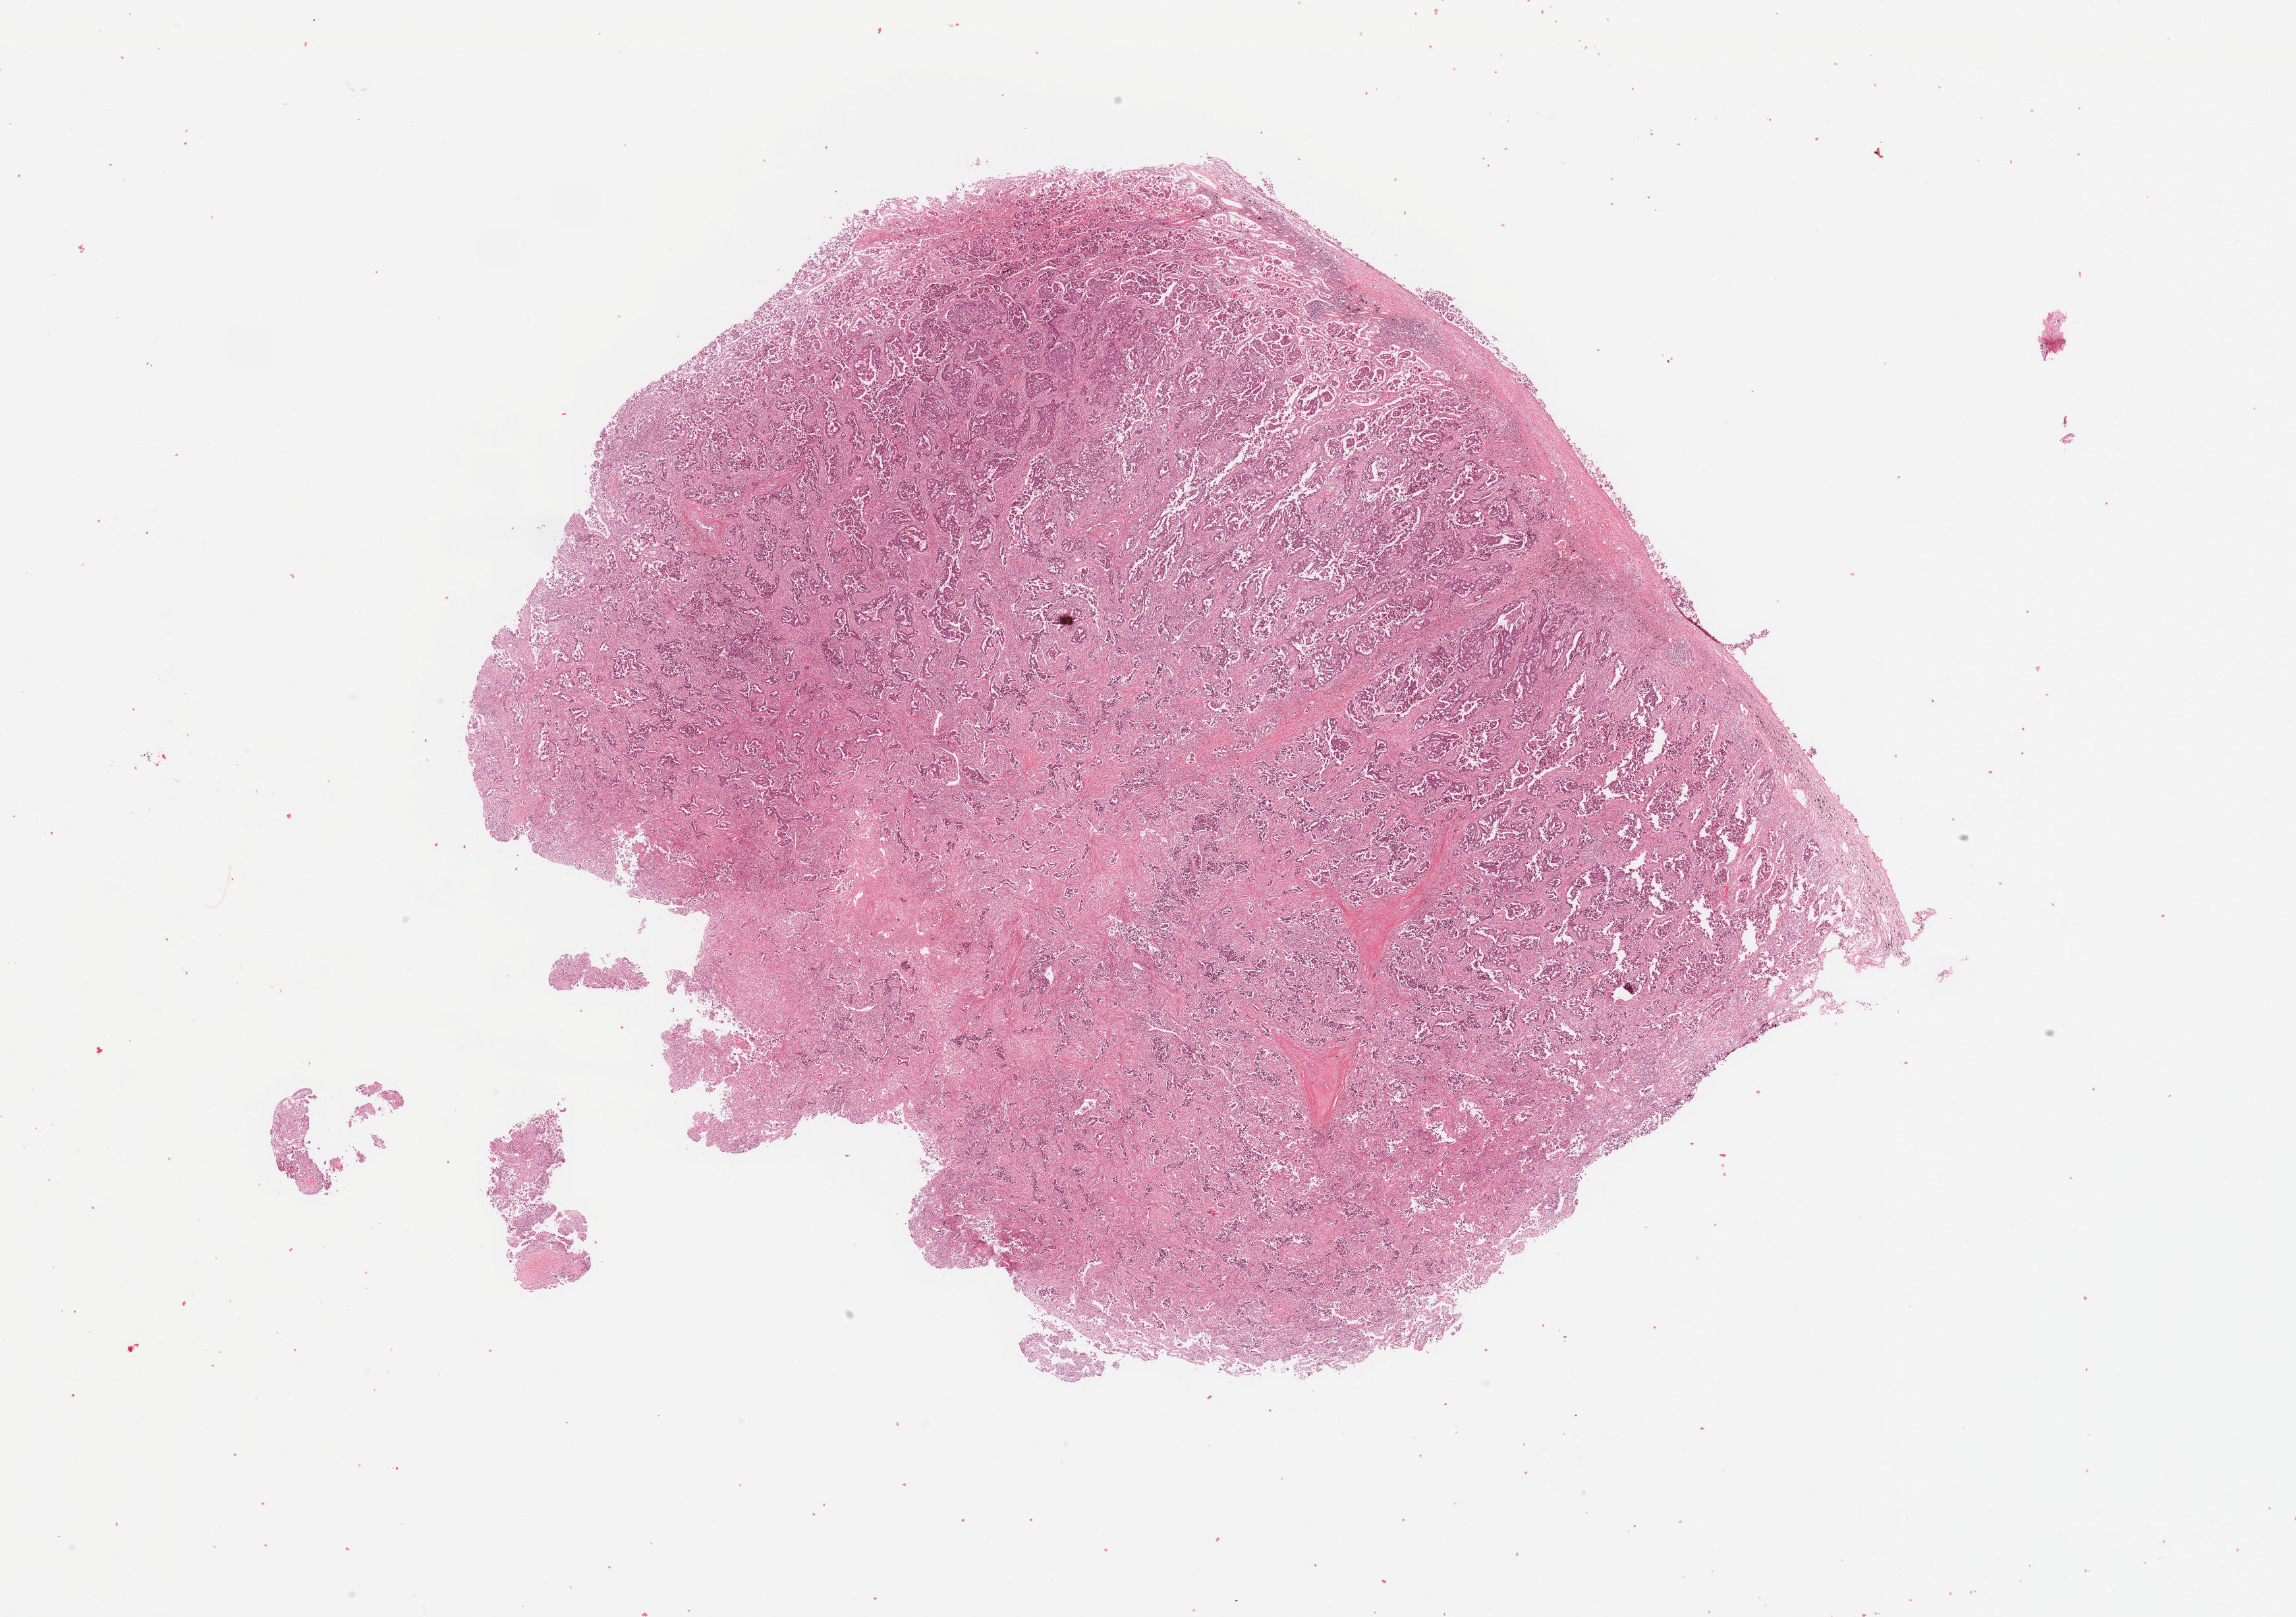
Digitized Hematoxylin and eosin (H&E) stained tissue section (whole slide), a low-resolution overview of the entire scanned area, about 27.6 x 19.4 mm (acquisition: 20x scan), tumour tissue sample, sampled site: lung. Patient: male, age 62 years. Histologic grade: G3 (poorly differentiated). Pathologist review of this section (percent, as recorded): tumour nuclei 65%, necrosis 5%.
• primary tumour site (as recorded): left upper lobe
• histologic diagnosis: Adenocarcinoma, NOS
• AJCC pathologic stage: IIIA